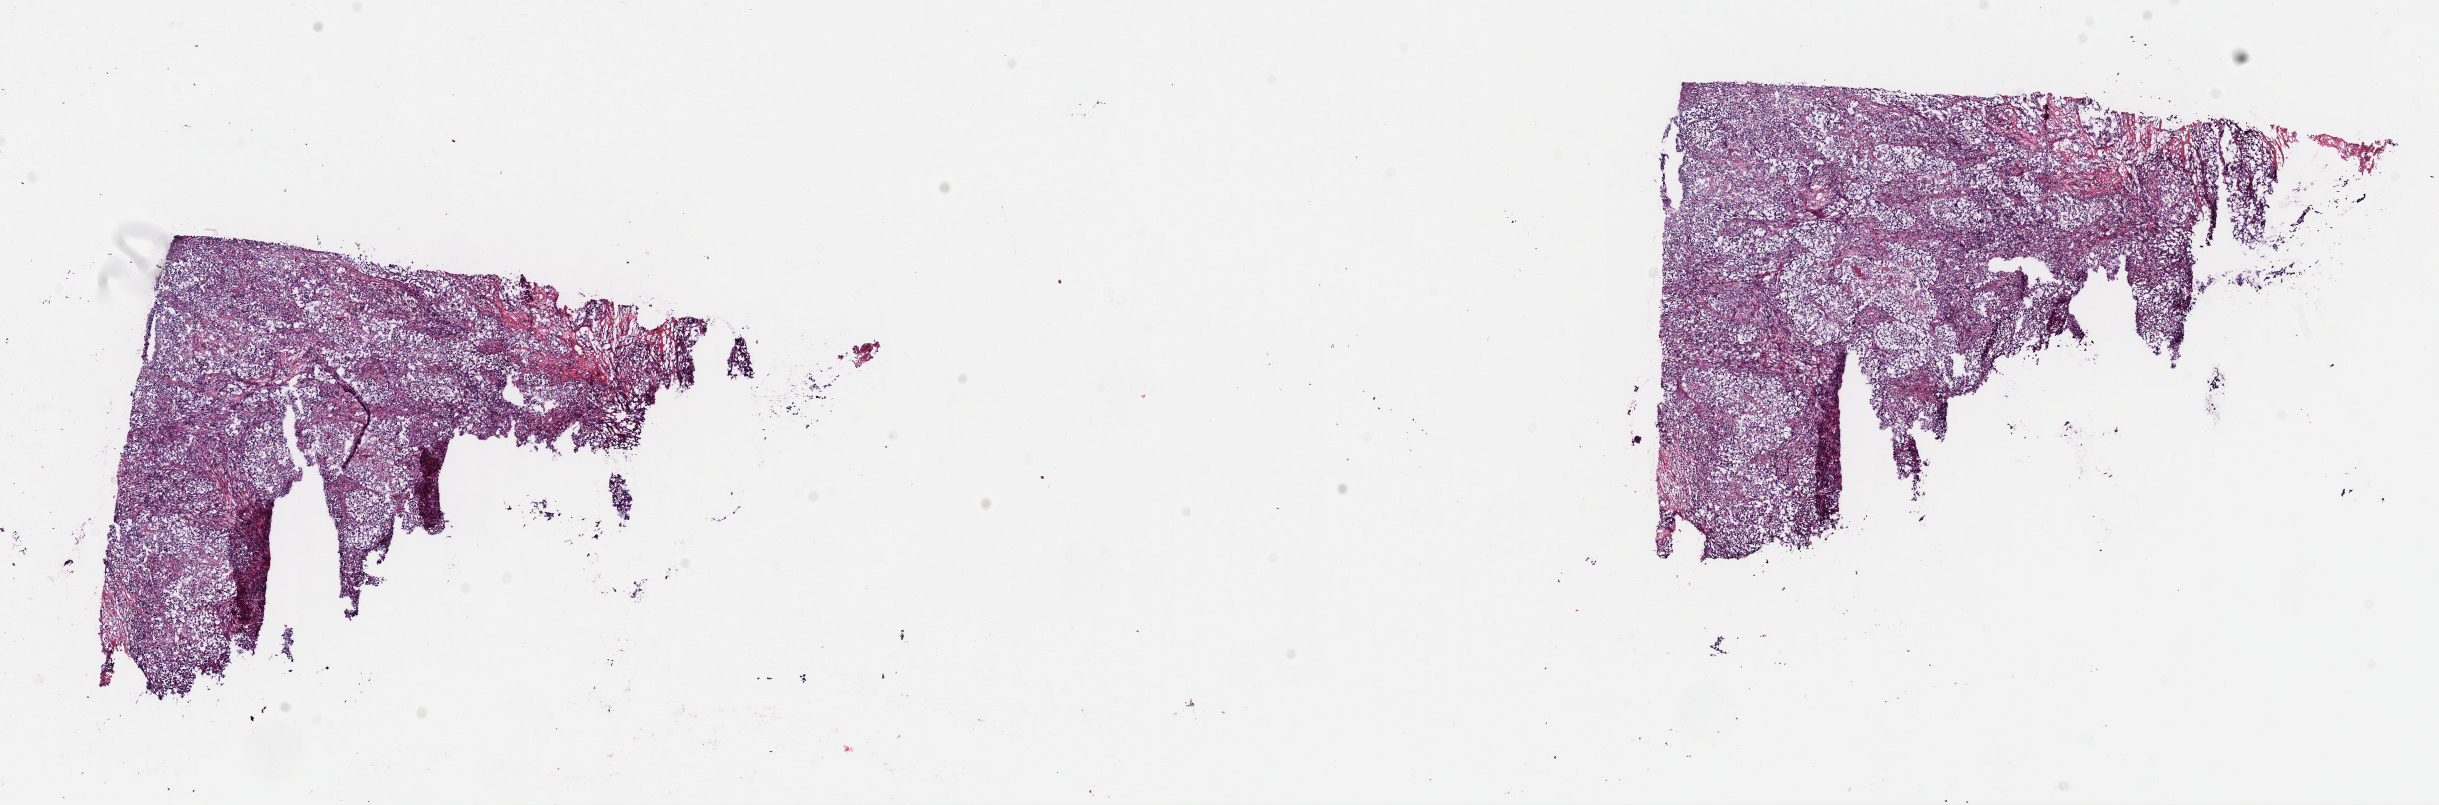
H&E whole-slide image — low-resolution overview of the scanned area, about 19.3 x 6.4 mm; frozen section from the top of the tissue portion; metastatic tumour sample, sampled site: lymph nodes of axilla or arm. Patient: female, age at initial diagnosis 53 years. Composition of this section per pathologist review: tumour cells 77%, tumour nuclei 80%, normal cells 0%, stromal cells 20%, necrosis 3%. Infiltration values recorded for this section: lymphocyte infiltration 5%, monocyte infiltration 0%, neutrophil infiltration 0%.
This section: metastatic tumour tissue. Patient diagnosis: Malignant melanoma, NOS.